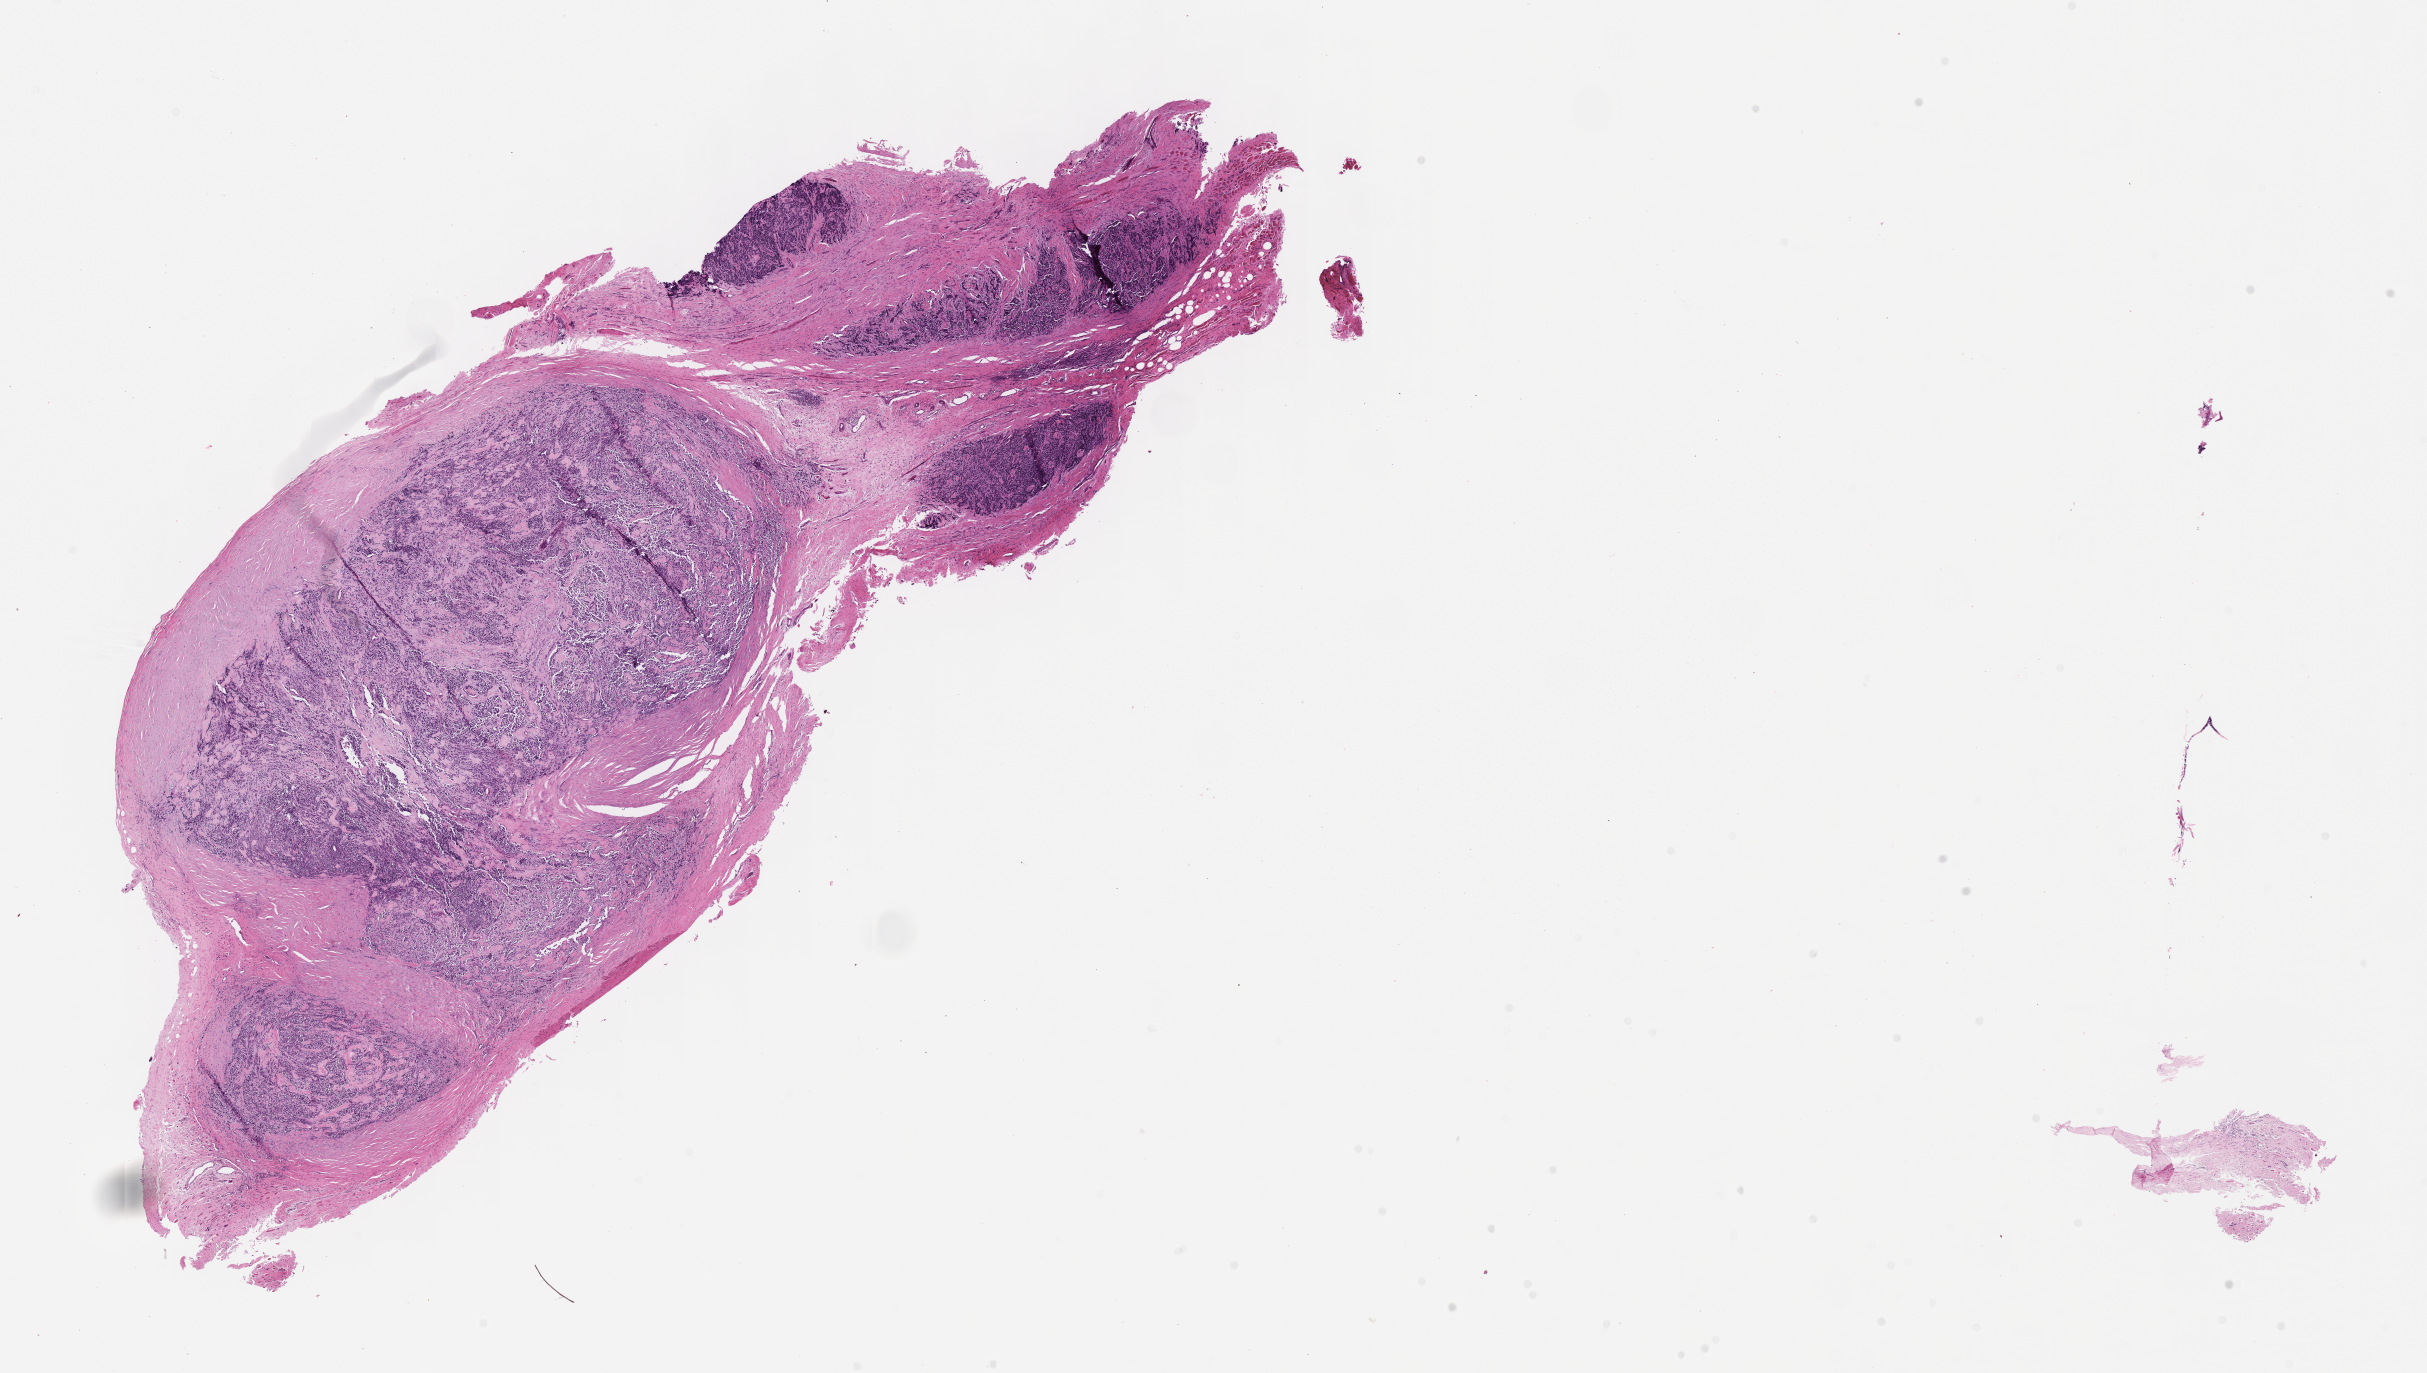
Whole-slide image, hematoxylin and eosin (H&E) stain of tumor tissue — low-resolution overview of the scanned area, about 19.6 x 11.1 mm; formalin-fixed paraffin-embedded section; sample anatomic site: arm, left. Male patient, age at diagnosis 11.1 years.
Stage (as recorded): 4. Metastatic status at presentation (as recorded): metastatic (confirmed). Diagnosis: rhabdomyosarcoma; histological classification: alveolar rhabdomyosarcoma.